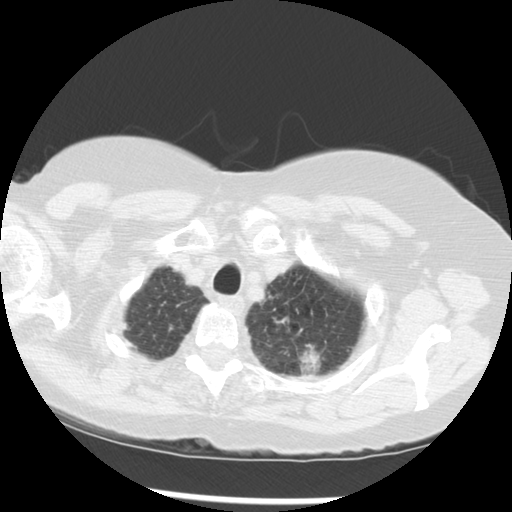
Chest CT (low-dose screening protocol), one axial image; third screening round (two years after baseline); lung window (W 1500 / L -600 HU); 2.5 mm slice thickness; standard (soft-tissue) reconstruction kernel (STANDARD); slice 249 of 283 in the series. Female participant, aged 70 years at enrolment.
Expert-annotated lung lesion, bounding box <242,297,342,384> (left, top, right, bottom; pixels). The exam's reader record, not a measurement of the box and not confirmed to be the same lesion: non-calcified nodule or mass ≥4 mm, left upper lobe, 32 × 26 mm, spiculated (stellate) margins, soft tissue attenuation, pre-existing on the prior screen: yes; interval growth: yes. Official screen result: positive, other. Later outcome: lung cancer diagnosed 24 days after this screen — neoplasm, malignant, left upper lobe, stage IIIB (AJCC 6th edition), 40 mm at pathology.